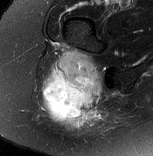
MRI of an extremity soft-tissue mass, one axial slice. Slice 50 of 77 in the series (ordered by position). T2-weighted fat-saturated. MR volume resampled by the dataset authors to the PET/CT grid (not the native acquisition matrix). 153 × 156 image matrix, field of view 149 × 152 mm. Female patient. Case-level facts recorded for this patient, not image findings: histological type: synovial sarcoma; grade: intermediate; site of the primary tumour: right buttock.
Outlined on this slice (expert contour drawn on MRI and transferred to this co-registered scan by the dataset authors):
- gross tumour volume including surrounding oedema: bounding box [x1, y1, x2, y2] px = [44, 52, 106, 130]
- gross tumour volume (mass): [44, 52, 102, 117]